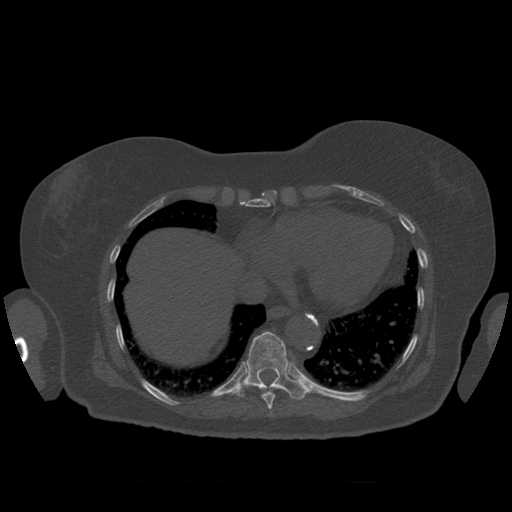
CT including the spine, one axial slice; position 347 of 399 along the scan axis; 120 kVp; bone window (W 1800 / L 400 HU); 1.25 mm slice thickness; 512 × 512 image matrix, field of view 404 × 404 mm. Patient age 81 years. From the clinical record (not read from this slice): primary cancer: renal.
Outlined on this slice (semi-automatic segmentation, software-assisted and operator-edited):
- T10 vertebra: bounding box (x1, y1, x2, y2) in pixels: (232, 332, 308, 400)
- T9 vertebra: (262, 390, 275, 410)